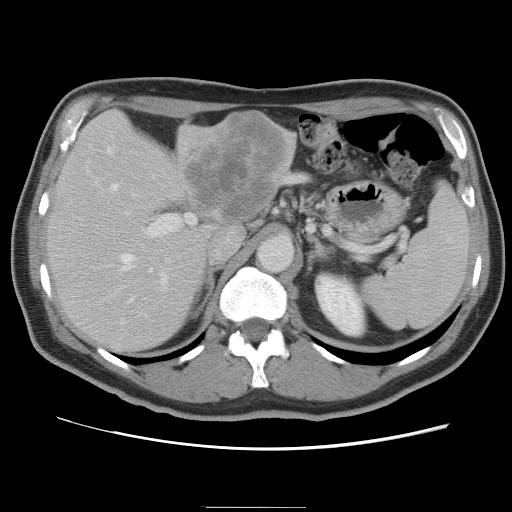
Contrast-enhanced abdominal CT, one axial slice; slice 52 of 87 in the series (ordered by position); 120 kVp; intravenous contrast given; soft-tissue window (W 400 / L 40 HU); 512 × 512 image matrix. Male patient, age 63 years. Case-level facts recorded for this patient, not image findings: diagnosis: colorectal cancer liver metastases, imaged before liver resection; multiple liver metastases: no; largest metastasis: 9 cm; disease in both lobes: no.
Annotated regions visible in this slice (manually delineated by an expert):
- hepatic veins: bounding box [x1, y1, x2, y2] px = [108, 148, 153, 303]
- liver: [47, 113, 296, 355]
- planned liver remnant (the part of the liver to remain after resection): [47, 146, 205, 355]
- portal vein (with intrahepatic branches): [96, 181, 196, 316]
- liver metastasis: [186, 117, 284, 226]